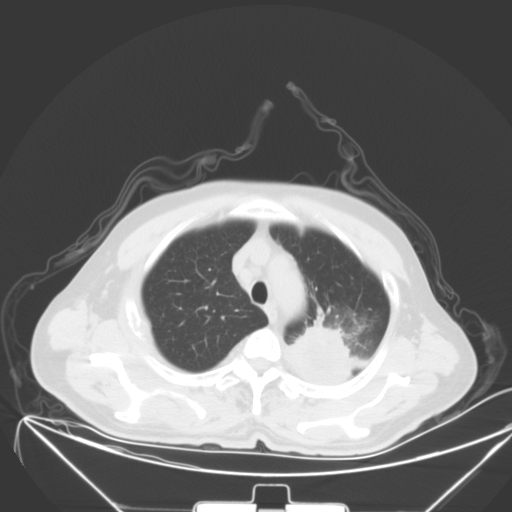
Chest CT, one axial slice. Slice 48 of 64 in the series (ordered by position). 120 kVp. Lung window (W 1500 / L -600 HU). 5 mm slice thickness. 512 × 512 image matrix, field of view 431 × 431 mm. Patient: male, 58 years. Case-level facts recorded for this patient, not image findings: clinical TNM (as recorded): T2b N3 M1b; histopathological grade: G3.
Annotated regions visible in this slice (rectangle marked by the reading radiologist):
- lung tumour (recorded histology: adenocarcinoma): bounding box (x1, y1, x2, y2) in pixels: (289, 317, 353, 391)